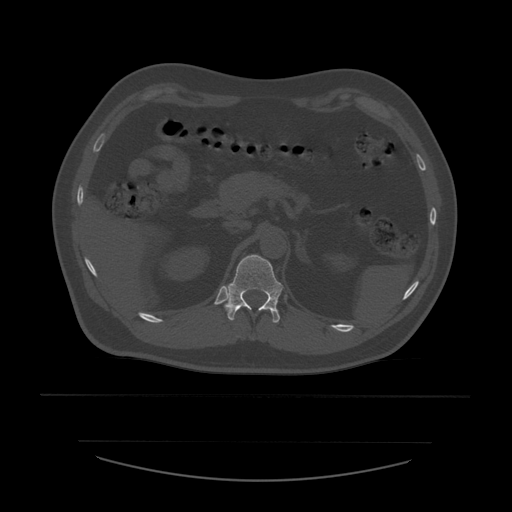
CT including the spine, one axial slice. Slice 256 of 532 in the series (ordered by position). Reconstruction kernel STANDARD. 120 kVp. Bone window (W 1800 / L 400 HU). 512 × 512 image matrix, field of view 441 × 441 mm. Patient age 44 years. From the clinical record (not read from this slice): primary cancer: soft tissue sarcoma.
Outlined on this slice (semi-automatic segmentation, software-assisted and operator-edited):
- T12 vertebra: box from (x=225, y=255) to (x=283, y=323) px